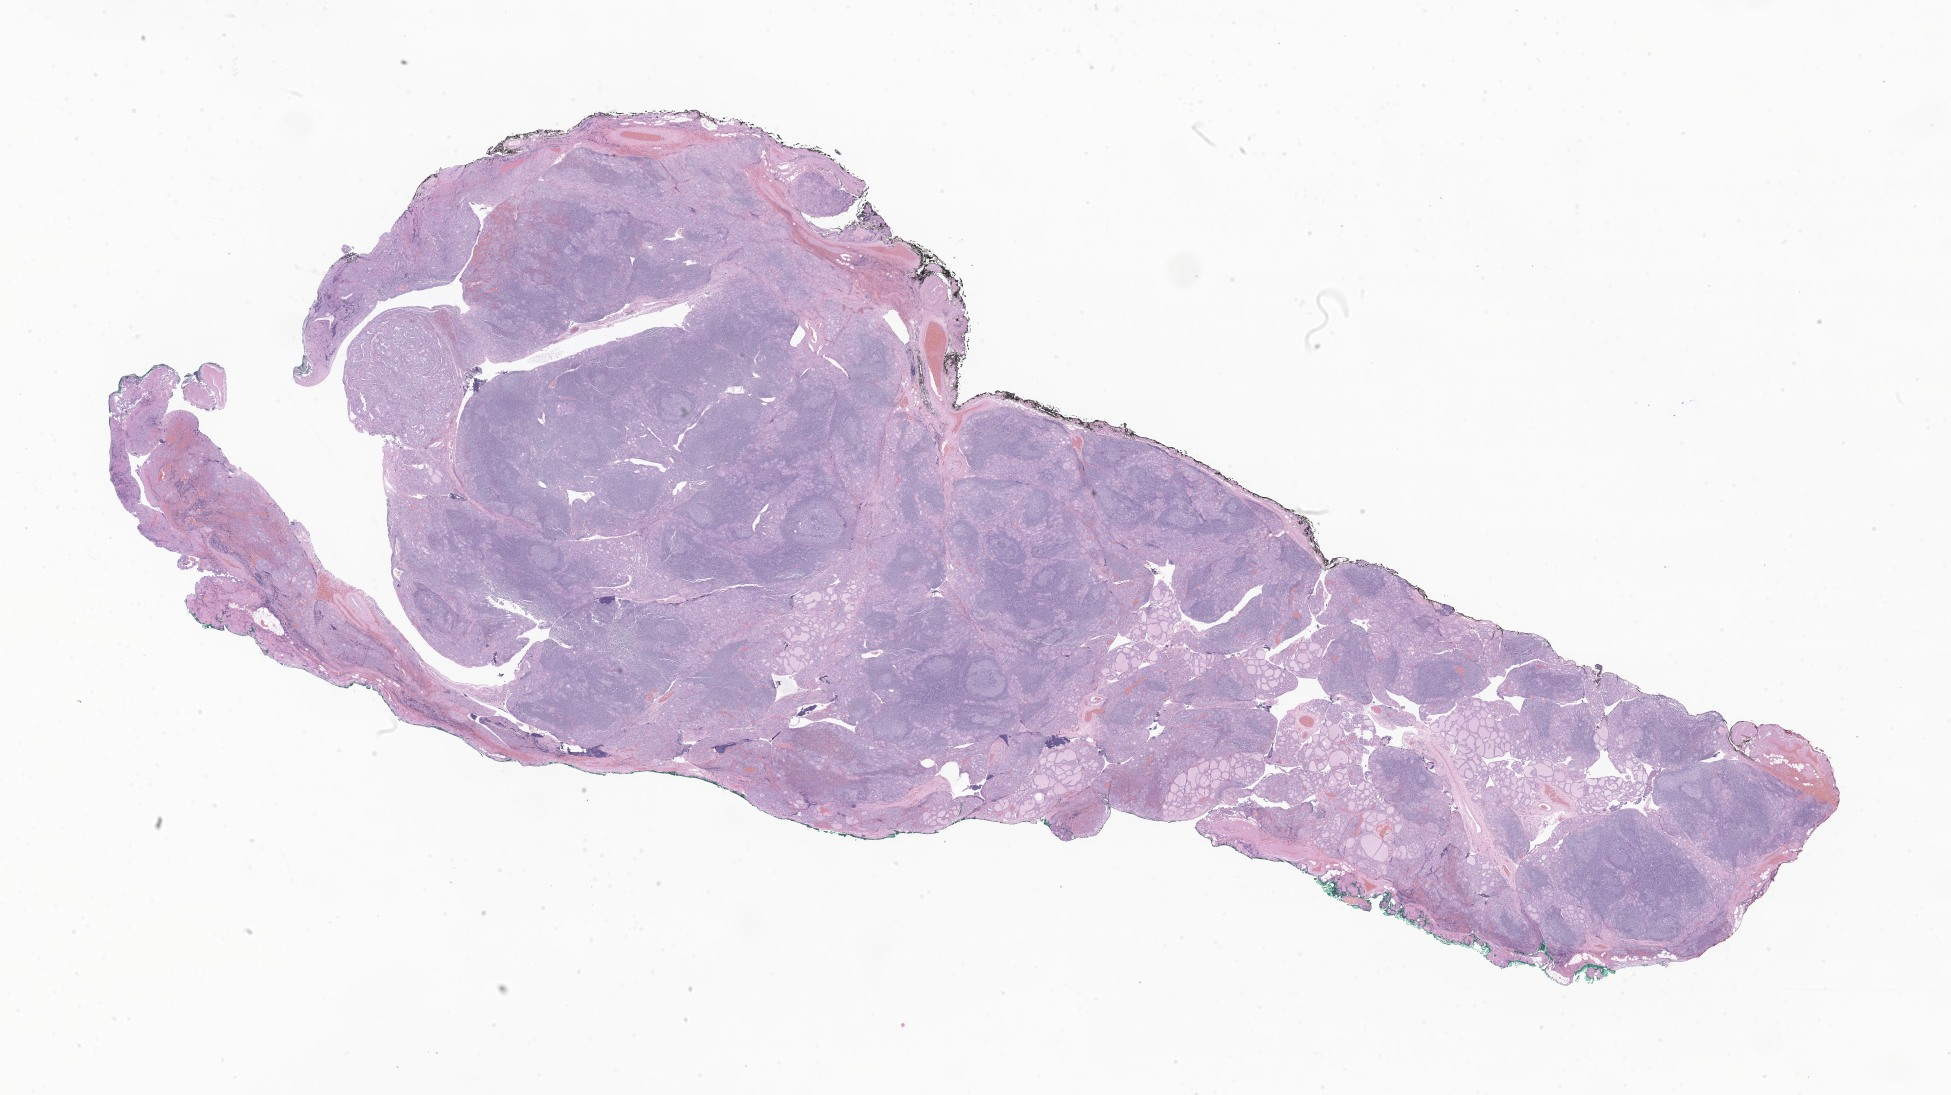
Hematoxylin and eosin (H&E) whole-slide image of tumor tissue from the thyroid, low-resolution overview of the scanned area, about 32.9 x 18.5 mm; formalin-fixed, paraffin-embedded (FFPE) tissue. Patient male; age 224 months (18 years 8 months).
Recorded diagnosis: Papillary adenocarcinoma, NOS.